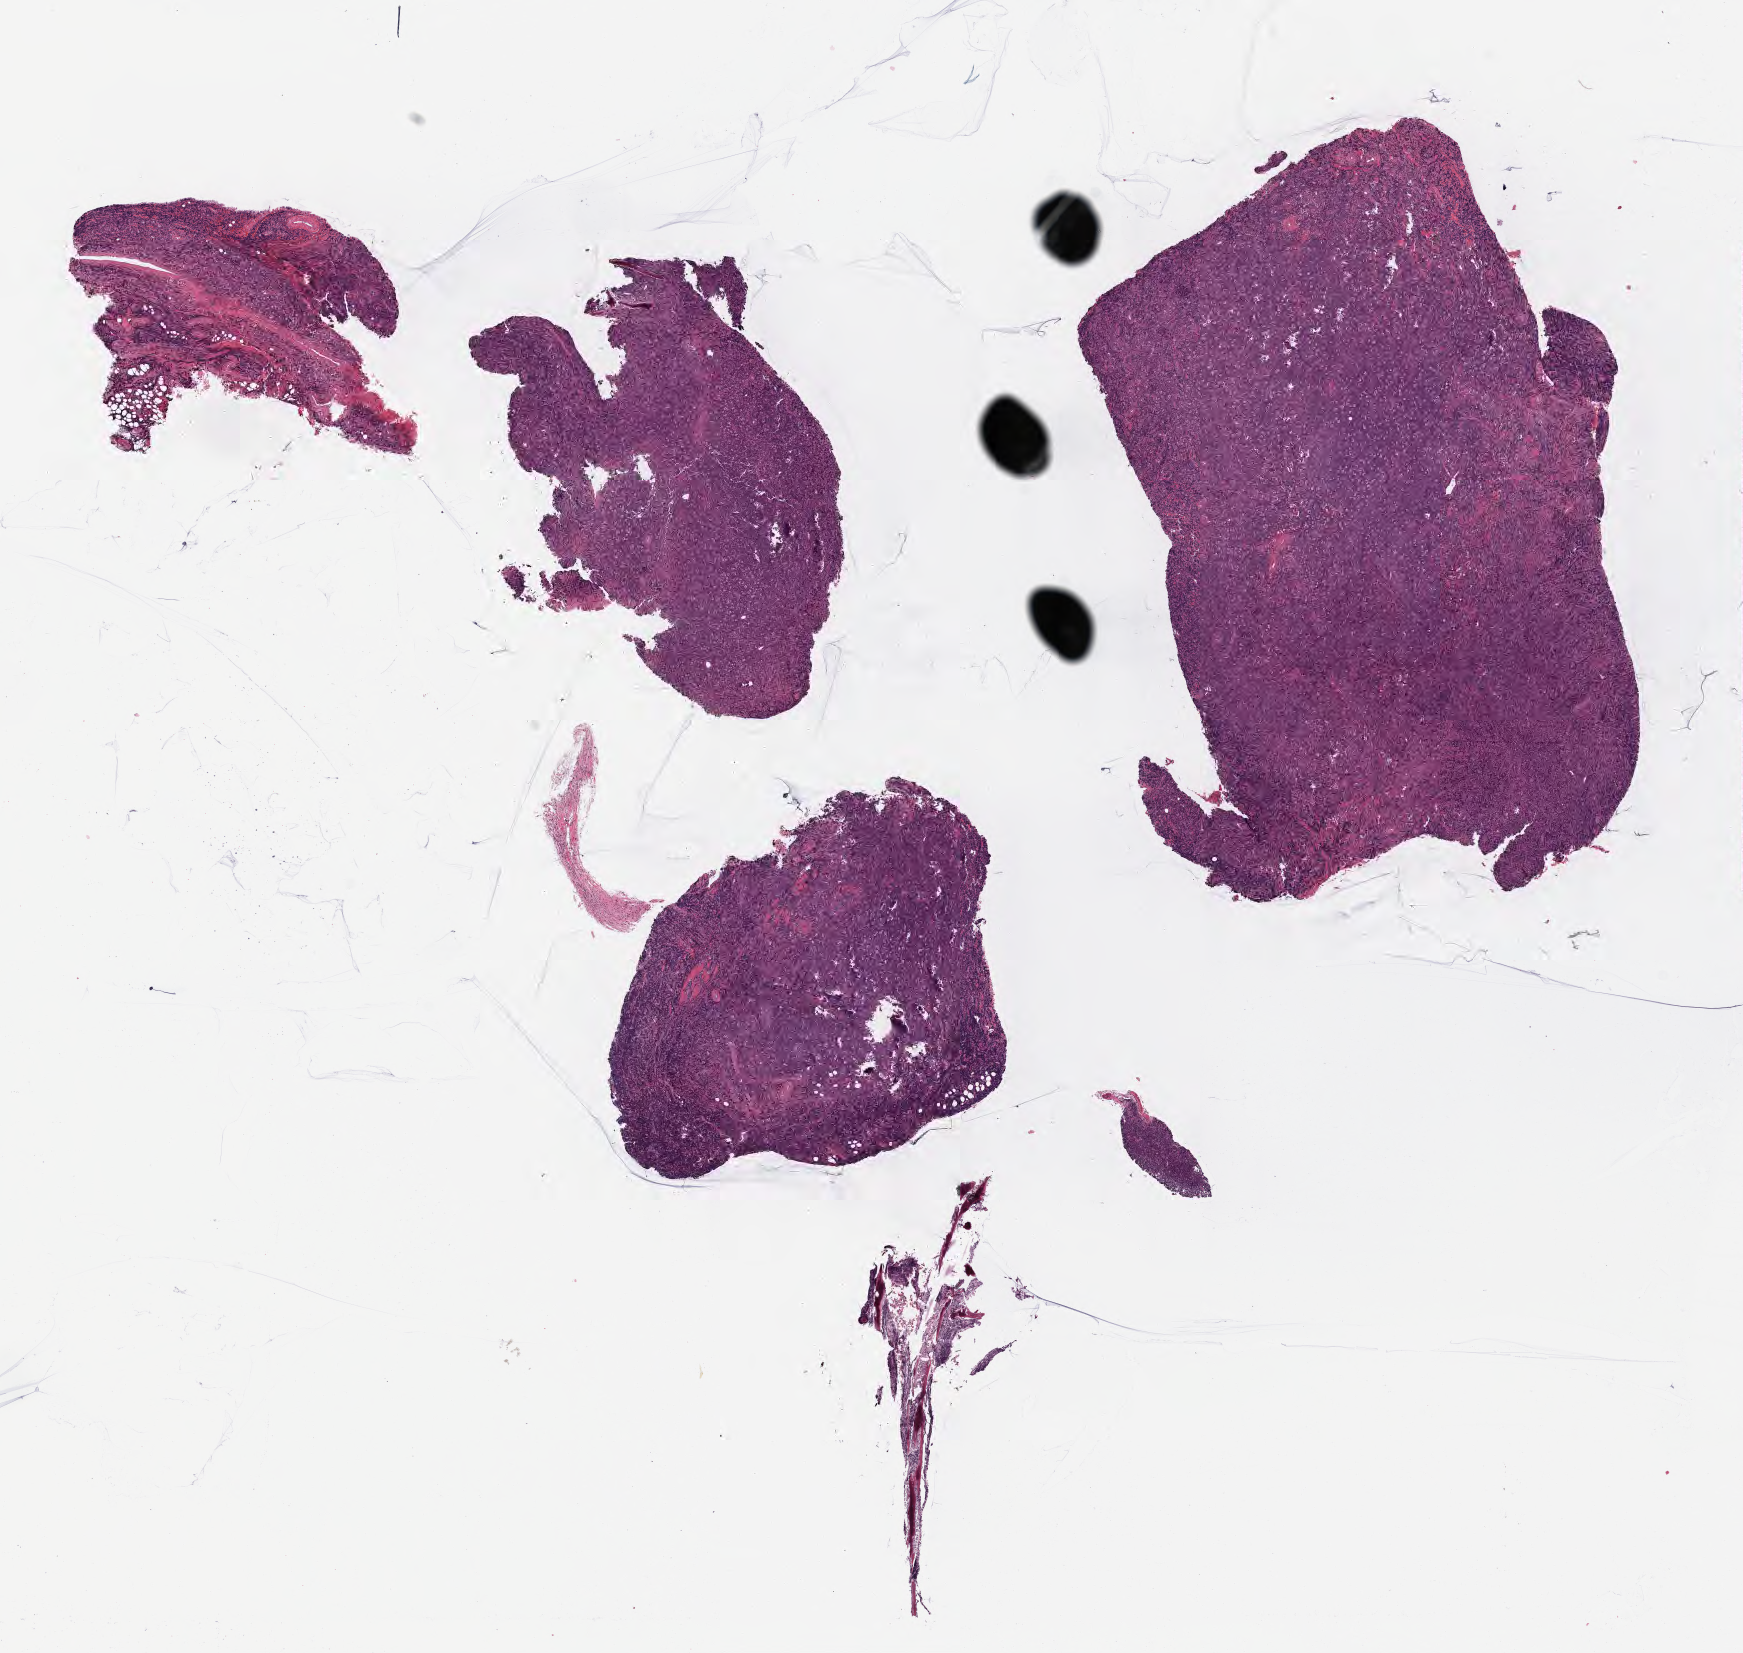
Haematoxylin and eosin whole-slide image, shown as a low-resolution overview of the whole scanned area (about 14.1 x 13.4 mm). Tumor tissue. Site: cranium. Patient female; age 10 years.
Histologic diagnosis: Diffuse large B-cell lymphoma, NOS.